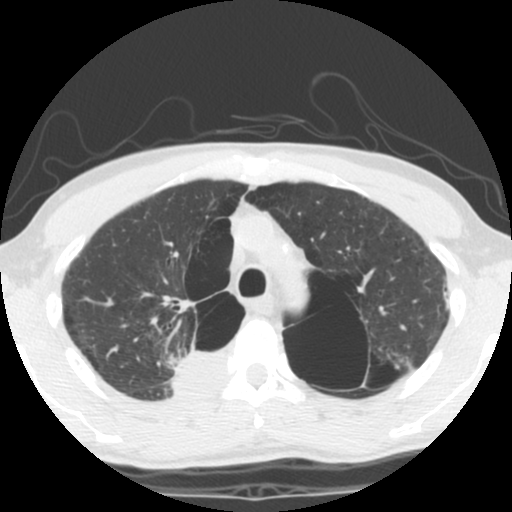
Low-dose screening chest CT, one axial slice. Position 87 of 119 along the scan axis. Reconstruction kernel STANDARD. Lung window (W 1500 / L -600 HU). 2.5 mm slice thickness. 512 × 512 image matrix, field of view 295 × 295 mm.
Structures marked on this image (manually delineated by an expert):
- lesion 1 (tumor, upper lobe of right lung): bounding box (x1, y1, x2, y2) in pixels: (174, 351, 228, 396)